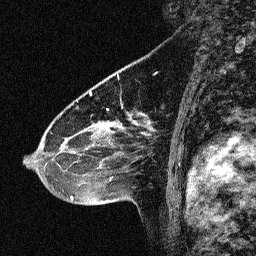
Breast MRI (dynamic contrast-enhanced), one sagittal slice; dynamic contrast-enhanced study with each time point stored as its own series, time point 2 of 3 at this slice position (early post-contrast, ordered by acquisition time); 1.5 T; TE 4.5 ms, TR 11 ms; 2.06 mm slice thickness; 256 × 256 image matrix, field of view 200 × 200 mm. Female patient, age 46 years. Case-level facts recorded for this patient, not image findings: setting: breast cancer imaged before/during neoadjuvant chemotherapy; receptor status: HER2-positive.
Outlined on this slice (semi-automatically segmented with operator editing):
- analysis volume of interest (the breast-tissue region the enhancement analysis was run in; not a lesion): bounding box (x1, y1, x2, y2) in pixels: (42, 80, 150, 180)
- tumour enhancement mask (voxels above the 90 % enhancement threshold inside the analysis volume of interest): (63, 113, 147, 142)